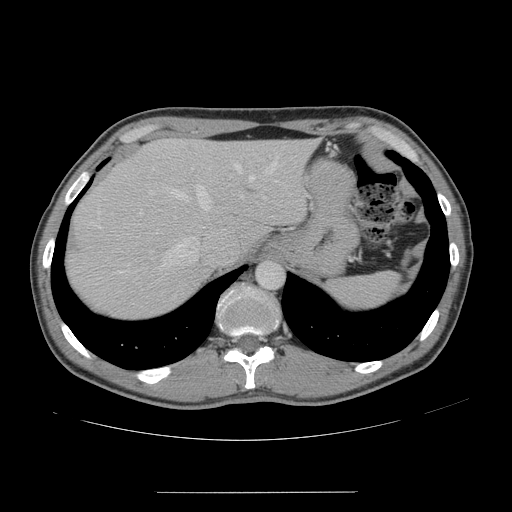
Contrast-enhanced abdominal CT, one axial slice; position 120 of 178 along the scan axis; intravenous contrast given; soft-tissue window (W 400 / L 40 HU); 2.5 mm slice thickness; 512 × 512 image matrix. Male patient, age 53 years. Case-level facts recorded for this patient, not image findings: diagnosis: colorectal cancer liver metastases, imaged before liver resection; multiple liver metastases: yes; largest metastasis: 2.4 cm; disease in both lobes: no.
Outlined on this slice (manually delineated by an expert):
- hepatic veins: bounding box [x1, y1, x2, y2] px = [151, 160, 276, 267]
- liver: [67, 139, 316, 319]
- planned liver remnant (the part of the liver to remain after resection): [149, 140, 315, 245]
- portal vein (with intrahepatic branches): [139, 210, 143, 215]